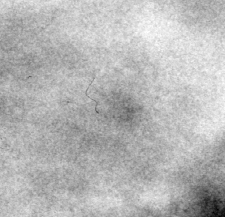
Cropped region of a digitized screen-film mammogram centred on a radiologist-marked abnormality; left breast; MLO view; BI-RADS breast density category 3 (scale 1–4).
- Finding: calcifications, morphology punctate, distribution segmental; BI-RADS assessment category 4; subtlety rating 3 on a 1 (subtle) to 5 (obvious) scale; pathology result (as recorded, not read from the image): benign.